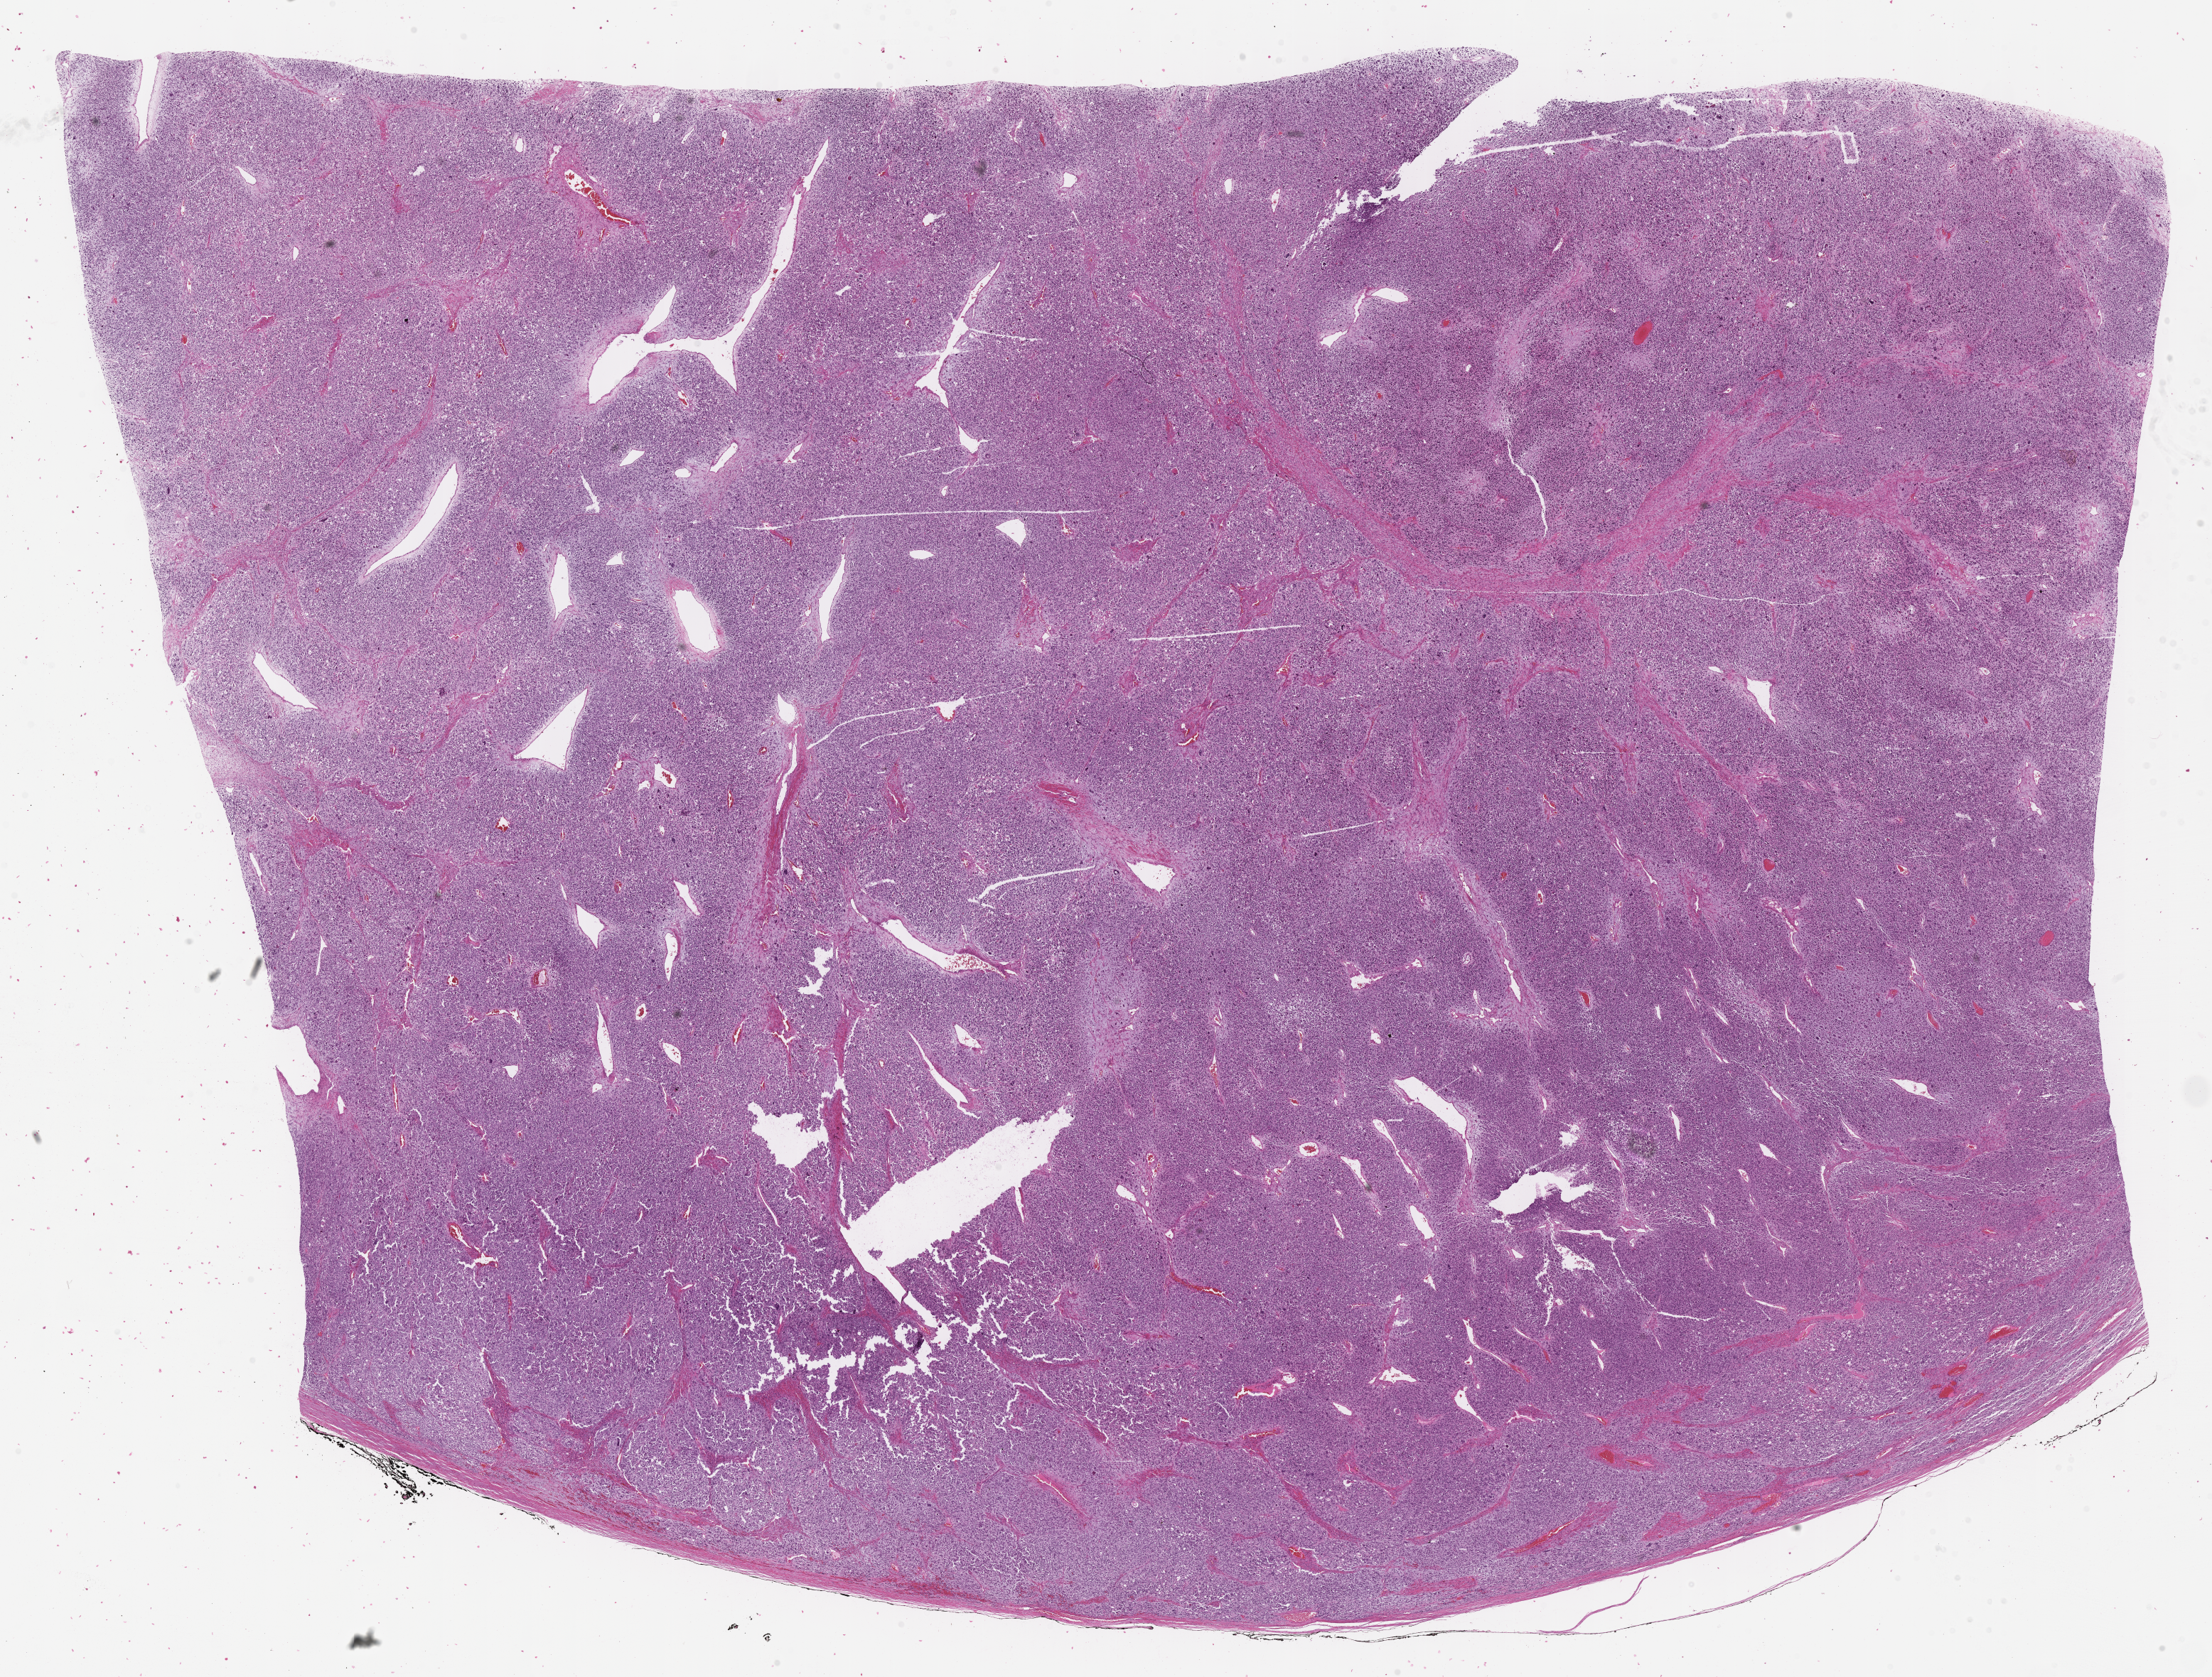
Whole-slide image, H&E stain of tumor tissue, low-resolution overview of the scanned area, about 25.2 x 19.1 mm, FFPE section, sample anatomic site: testicle-right. Male patient, age at diagnosis 14.6 years.
Primary site (case record): testis-Paratestis. Metastatic status at presentation (as recorded): non-metastatic. Stage (as recorded): 1. Diagnosis: rhabdomyosarcoma; histological classification: embryonal rhabdomyosarcoma.